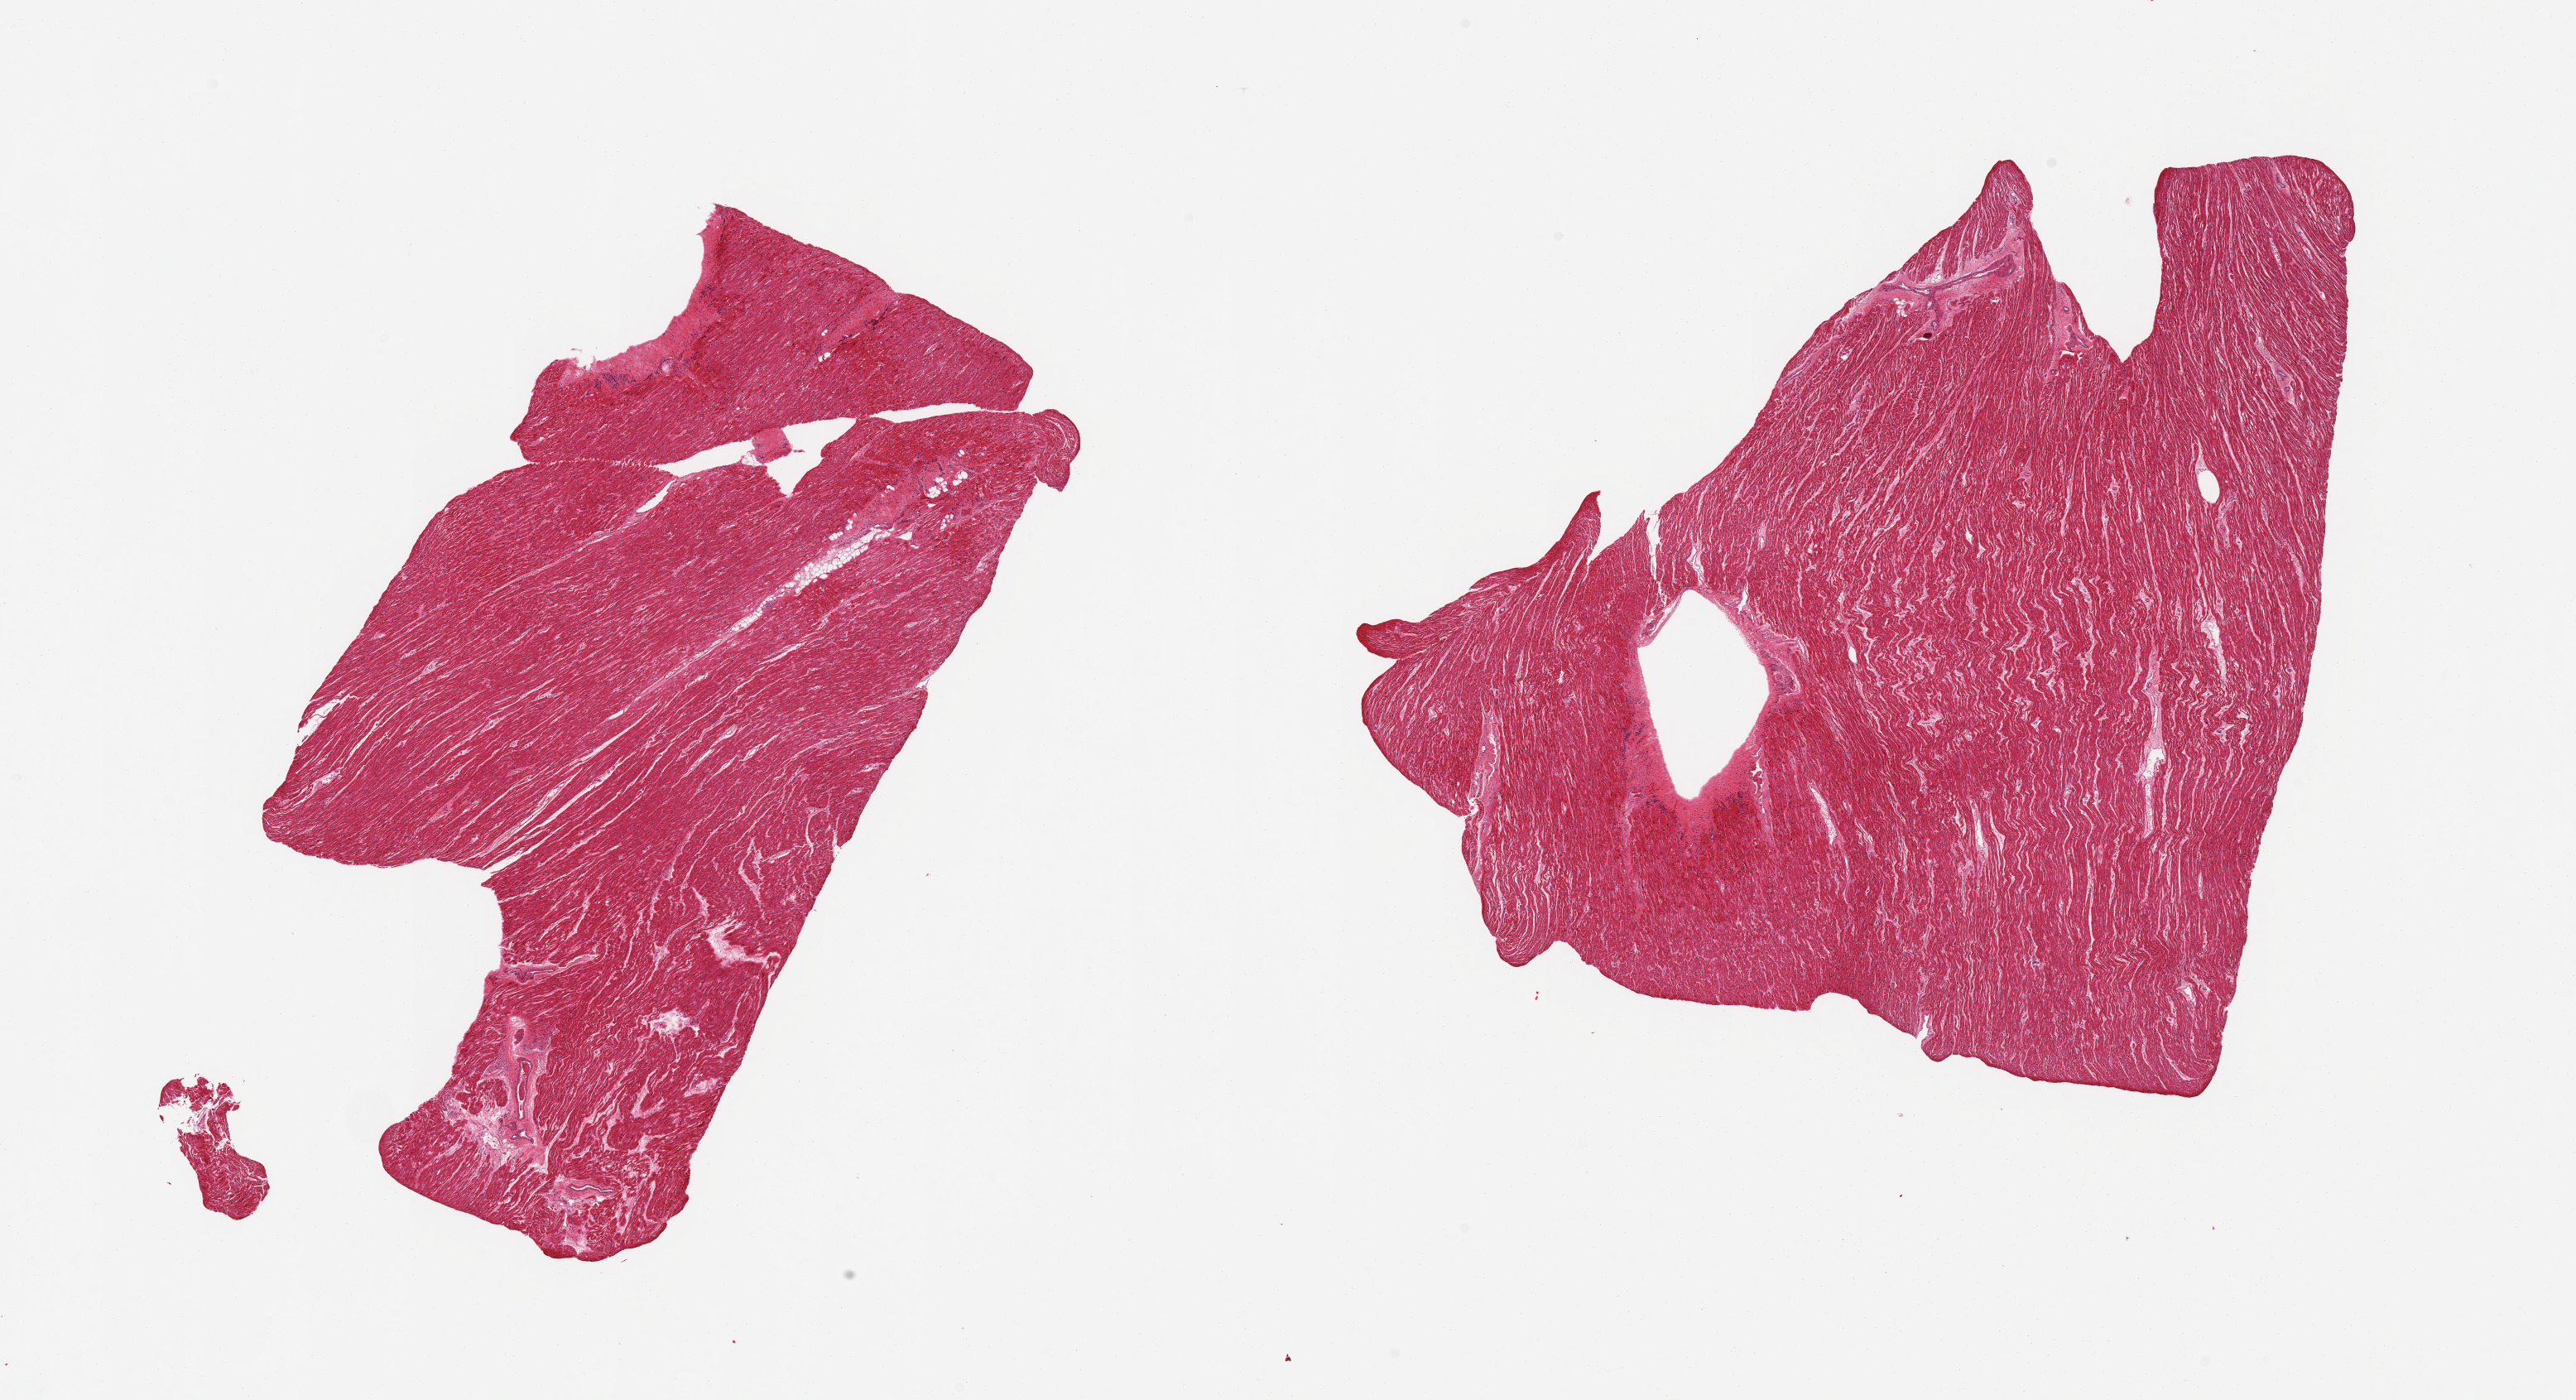
Digitized haematoxylin and eosin-stained section — a low-resolution overview of the entire scanned area, about 24.6 x 13.4 mm (acquisition: 20x scan), PAXgene-fixed paraffin-embedded (PFPE) section, section of heart (target tissue), tissue donor sample. Donor sex: female.
Review note (as recorded): 2 pieces; focal hypereosinophilia of fibers and ?degeneration (?early ischemia).